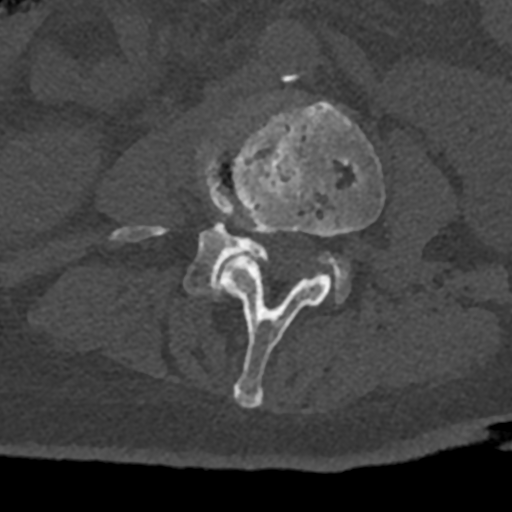
CT including the spine, one axial slice; reconstruction kernel Br40s/3; 120 kVp; bone window (W 1800 / L 400 HU); 512 × 512 image matrix, field of view 160 × 160 mm. Patient: male, 74 years. From the clinical record (not read from this slice): primary cancer: renal.
Outlined on this slice (semi-automatically segmented with operator editing):
- L3 vertebra: box from (x=221, y=101) to (x=385, y=408) px
- L4 vertebra: (x=113, y=146)–(x=349, y=303)